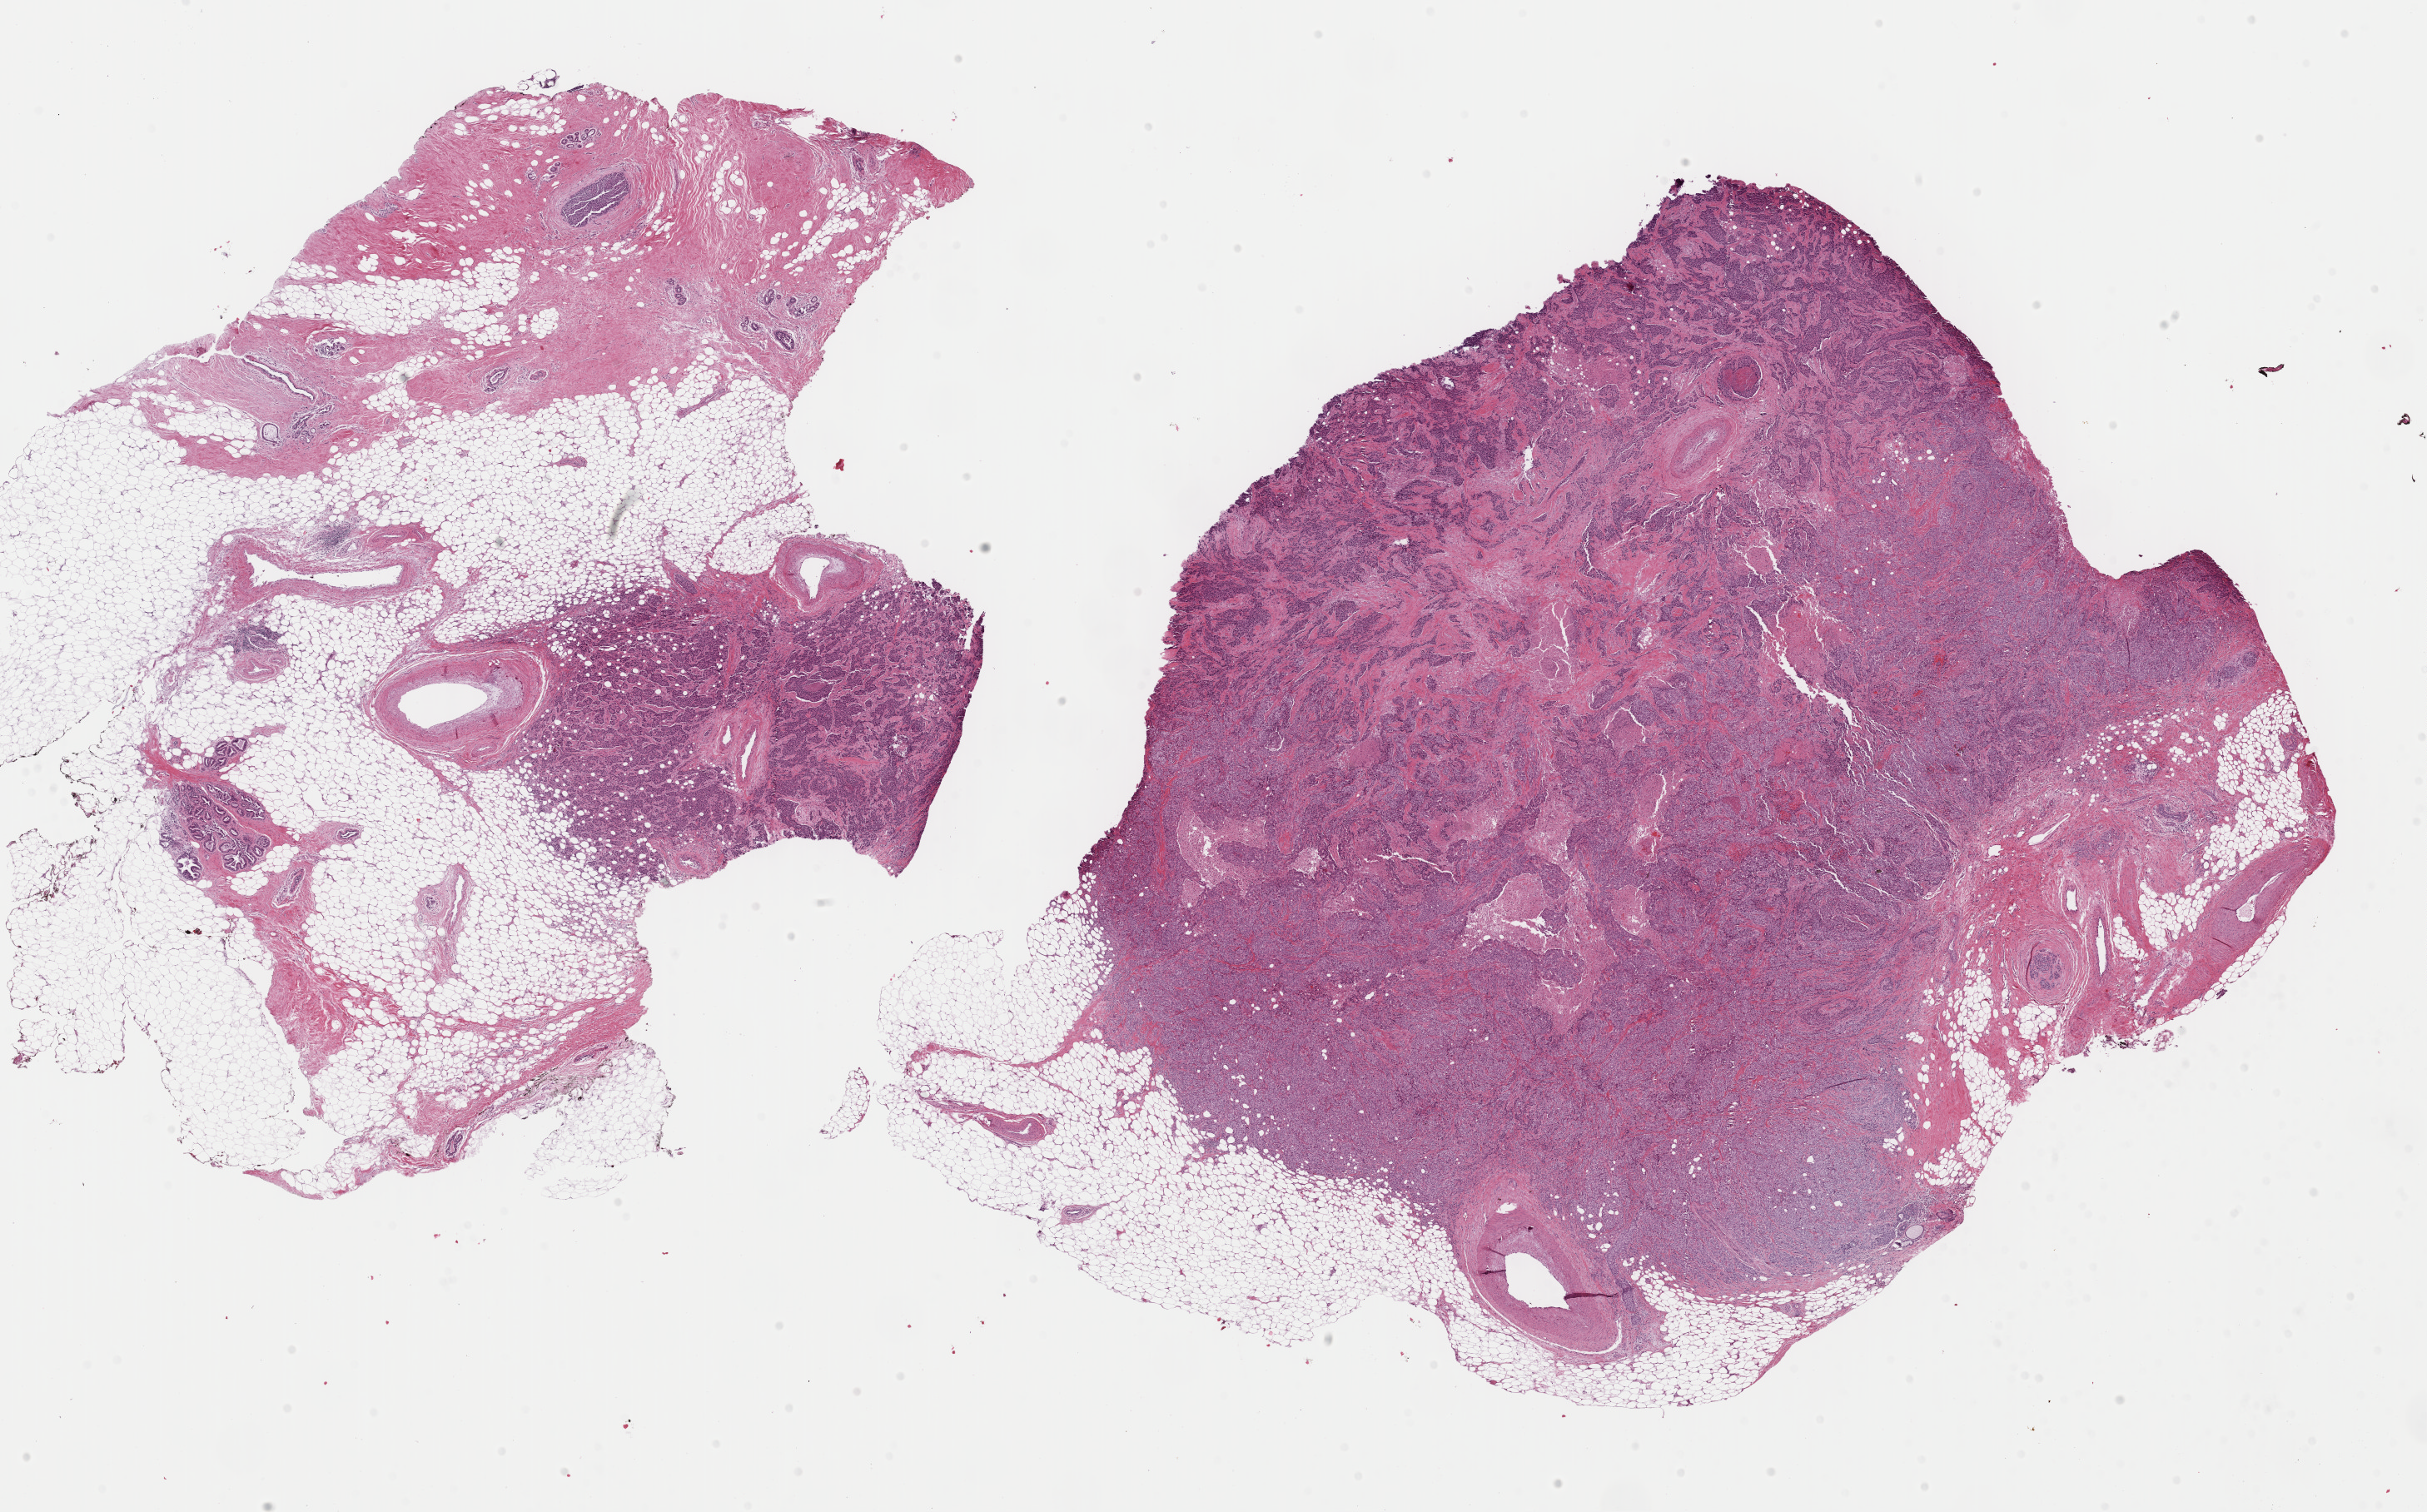
Whole-slide histology image, Hematoxylin and eosin (H&E) stained, whole scanned area (about 23.0 x 14.3 mm, from a 40x scan) shown as a low-resolution overview. Formalin-fixed paraffin-embedded (FFPE) diagnostic section. Sample: primary tumour, breast. Female, age 65 years at initial diagnosis.
- AJCC pathologic stage: I (6th edition)
- lymph nodes positive (case pathology): 0 of 4 examined
- TNM: T1 N0 M0
- pathologic diagnosis: Infiltrating duct carcinoma, NOS